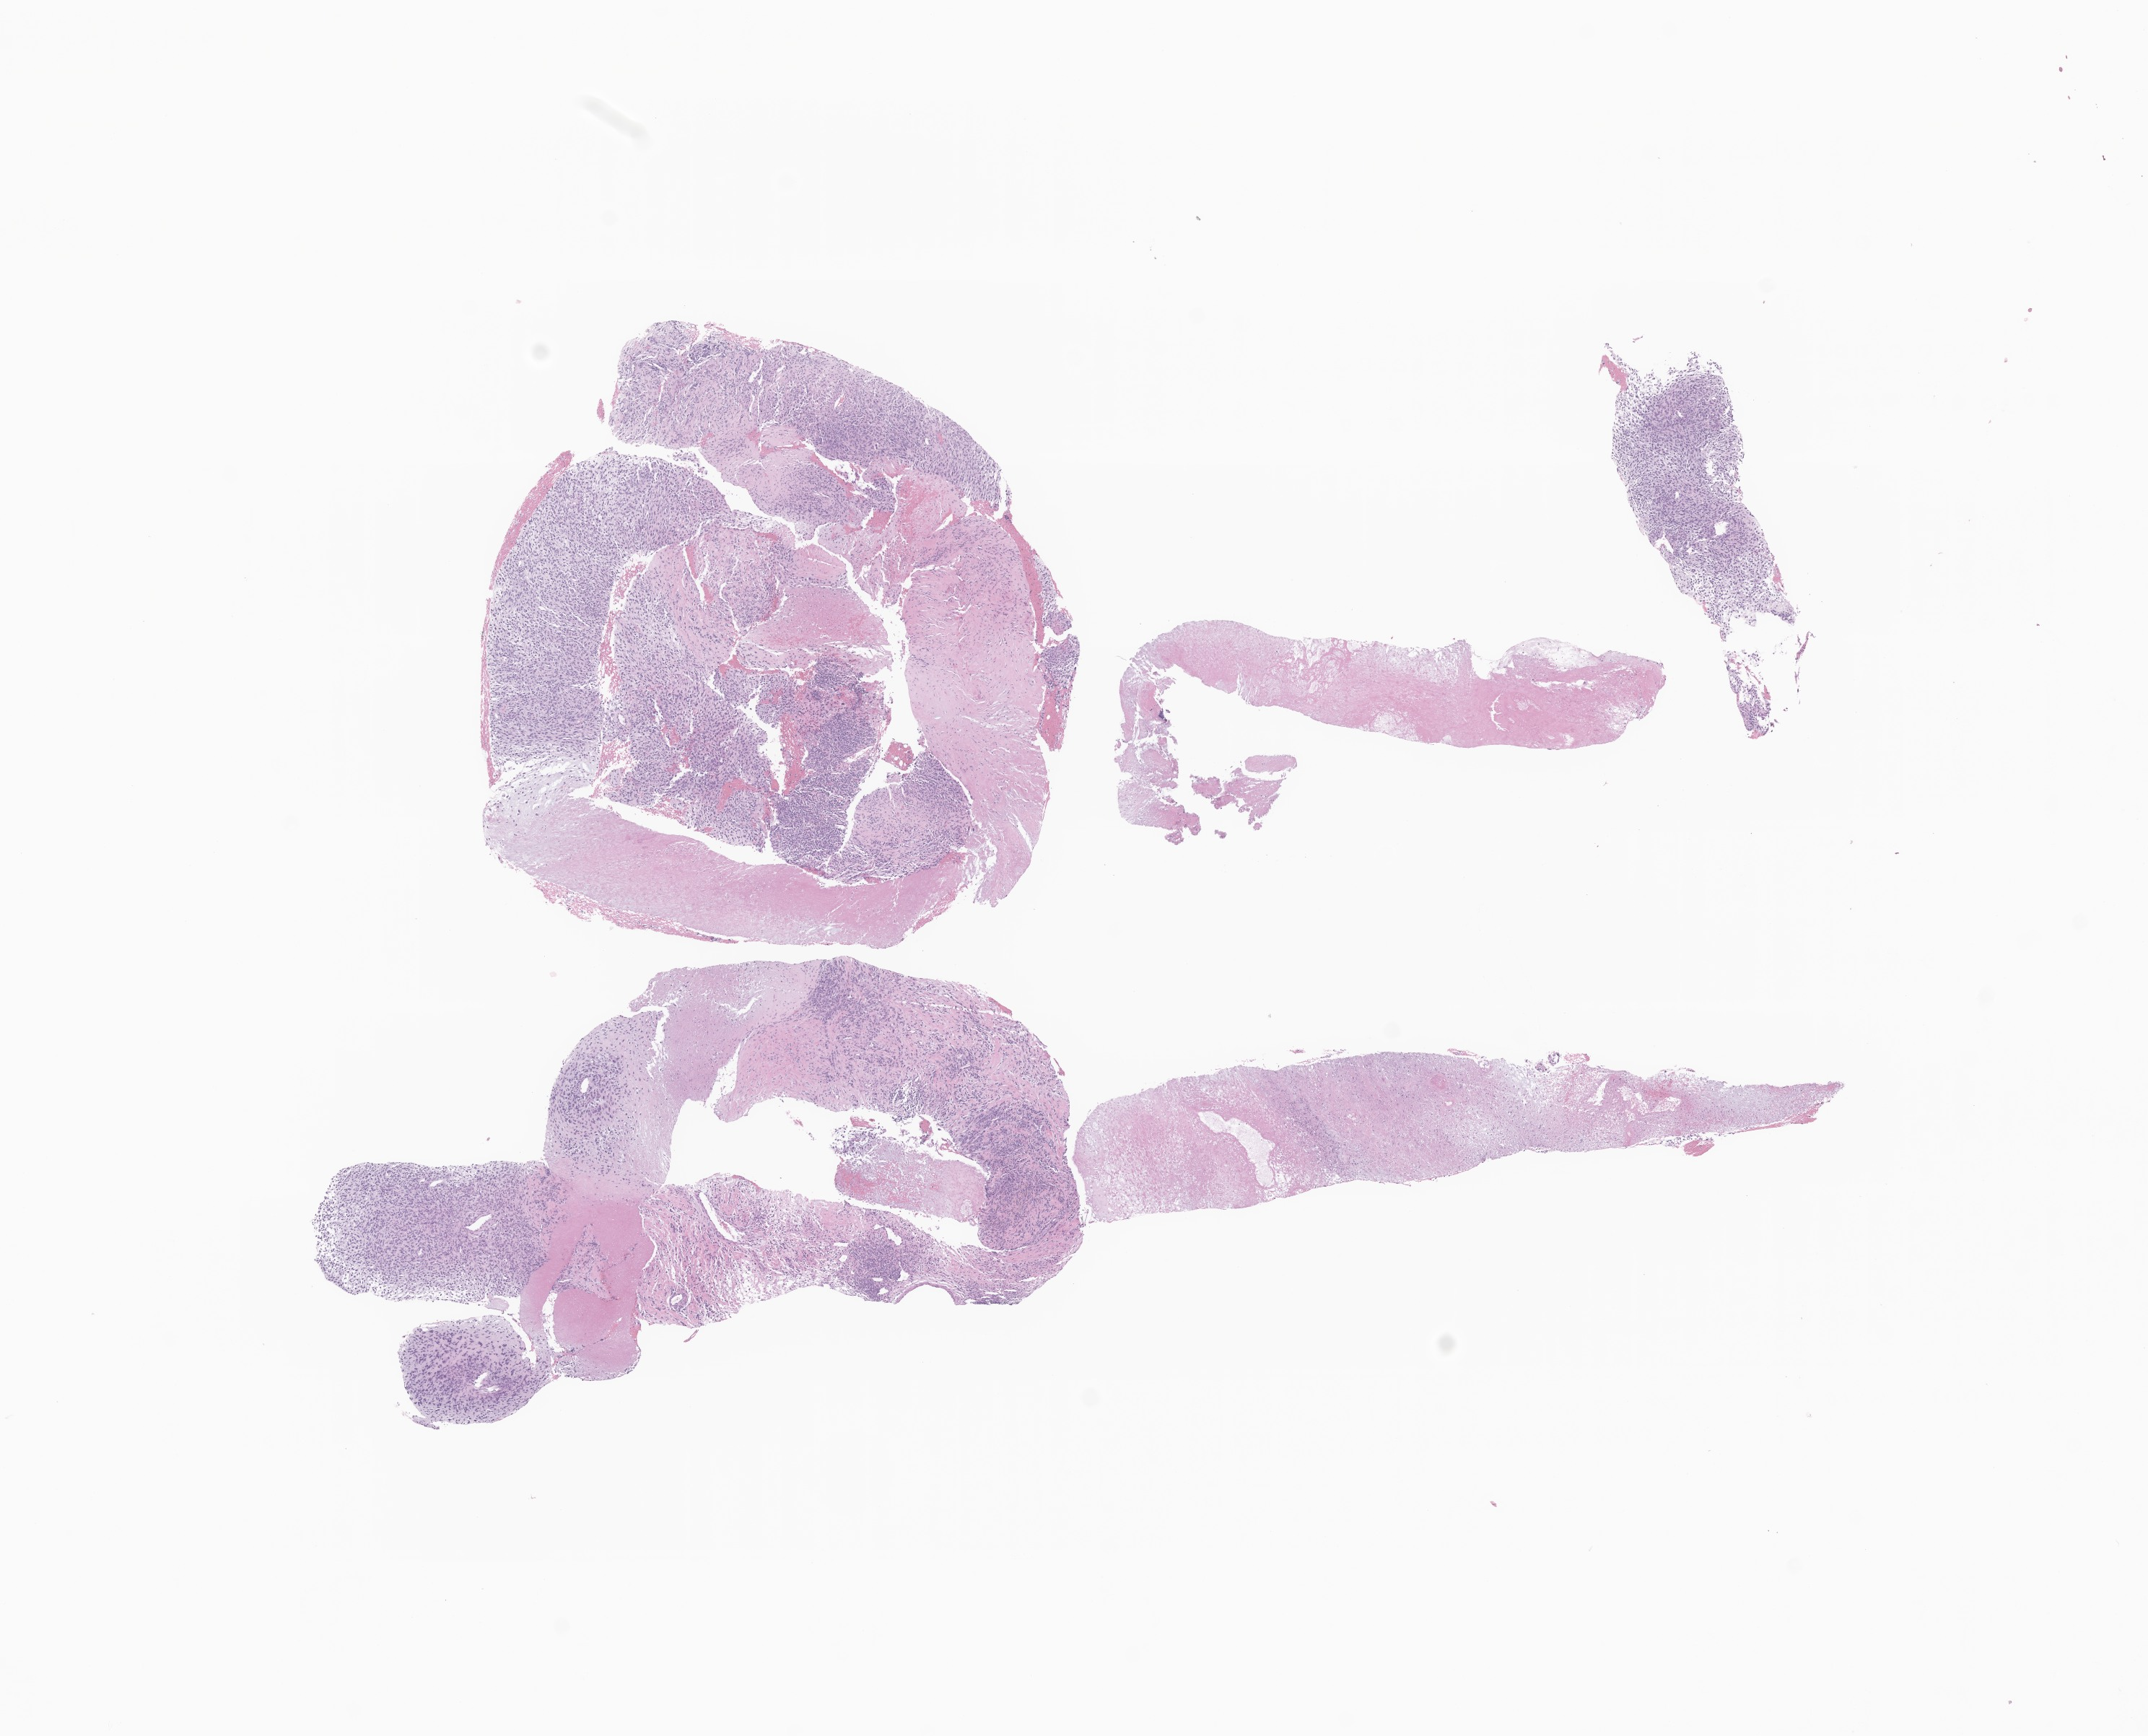
Digitized hematoxylin and eosin (H&E)-stained section of tumor tissue from the upper limb lymph node — shown as a low-resolution overview of the whole scanned area (about 12.5 x 10.1 mm); formalin-fixed paraffin-embedded section. Female patient, age 228 months (19 years).
• diagnosis (ICD-O-3 morphology term): Spindle cell sarcoma